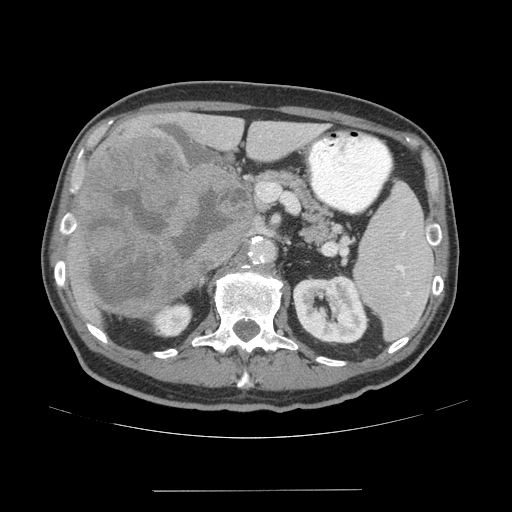
Contrast-enhanced abdominal CT (liver protocol), one axial slice; position 26 of 77 along the scan axis; reconstruction kernel STANDARD; 140 kVp; soft-tissue window (W 400 / L 40 HU); 2.5 mm slice thickness; 512 × 512 image matrix, field of view 400 × 400 mm. Case-level facts recorded for this patient, not image findings: diagnosis: hepatocellular carcinoma (patient treated with transarterial chemoembolisation; whether this scan precedes or follows treatment is not stated here); TNM stage (as recorded): Stage-IVA.
Structures marked on this image (semi-automatic segmentation, software-assisted and operator-edited):
- liver parenchyma outside the tumour (the mass and vessels are separate outlines, so this box may not span the whole liver): box from (x=66, y=112) to (x=322, y=318) px
- mass: (x=75, y=137)–(x=256, y=321)